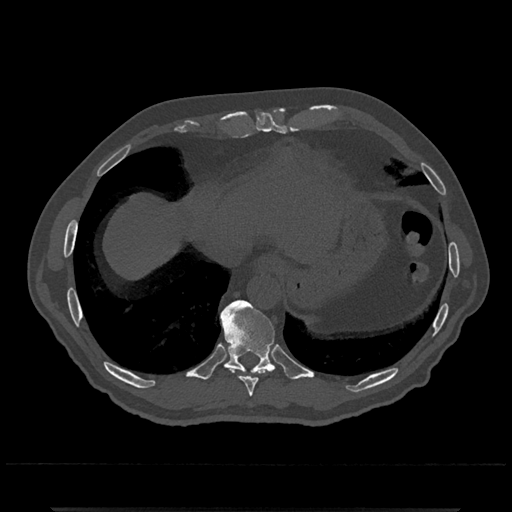
CT including the spine, one axial slice. Slice 581 of 797 in the series (ordered by position). 120 kVp. Bone window (W 1800 / L 400 HU). 512 × 512 image matrix, field of view 393 × 393 mm. Patient: male, 67 years. From the clinical record (not read from this slice): primary cancer: prostate.
Outlined on this slice (semi-automatic segmentation, software-assisted and operator-edited):
- T10 vertebra: bounding box <220,300,276,374> (left, top, right, bottom; pixels)
- T9 vertebra: <233,368,264,397>